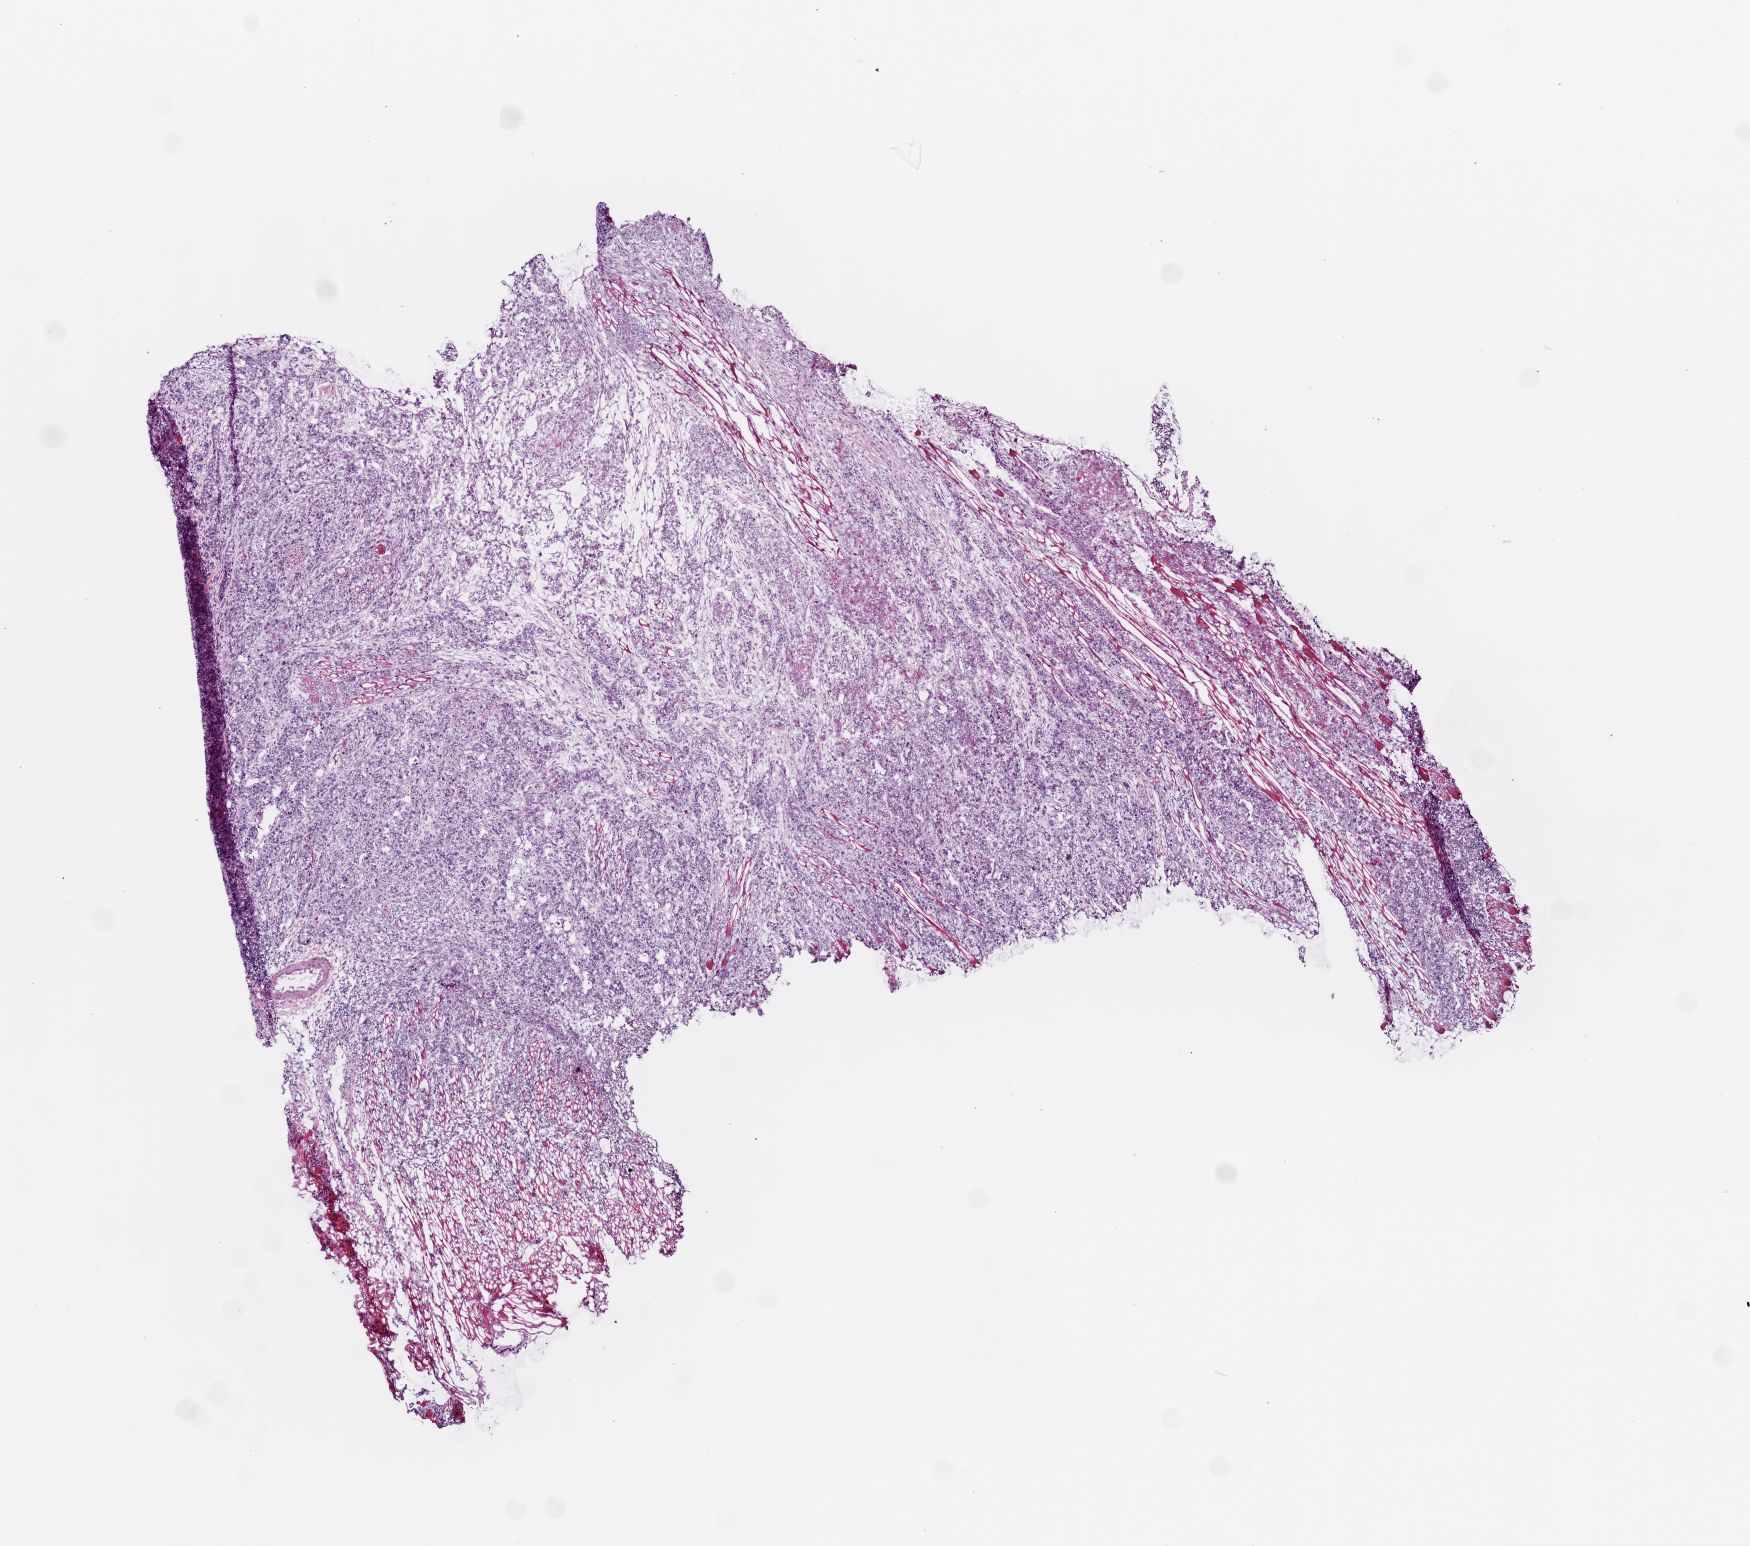
Whole-slide histology image, H&E — shown as a low-resolution overview of the whole scanned area (about 7.0 x 6.2 mm). Frozen section from the top of the tissue portion. Primary tumour sample from the head and neck. Female patient; age at initial diagnosis 69 years. Histologic grade: G3 (poorly differentiated). Composition of this section per pathologist review: tumour cells 100%, tumour nuclei 90%, necrosis 0%. Infiltration values recorded for this section: lymphocyte infiltration 2%, neutrophil infiltration 1%.
Histologic diagnosis: Squamous cell carcinoma, NOS (tongue, NOS). AJCC pathologic stage: IVA (6th edition).